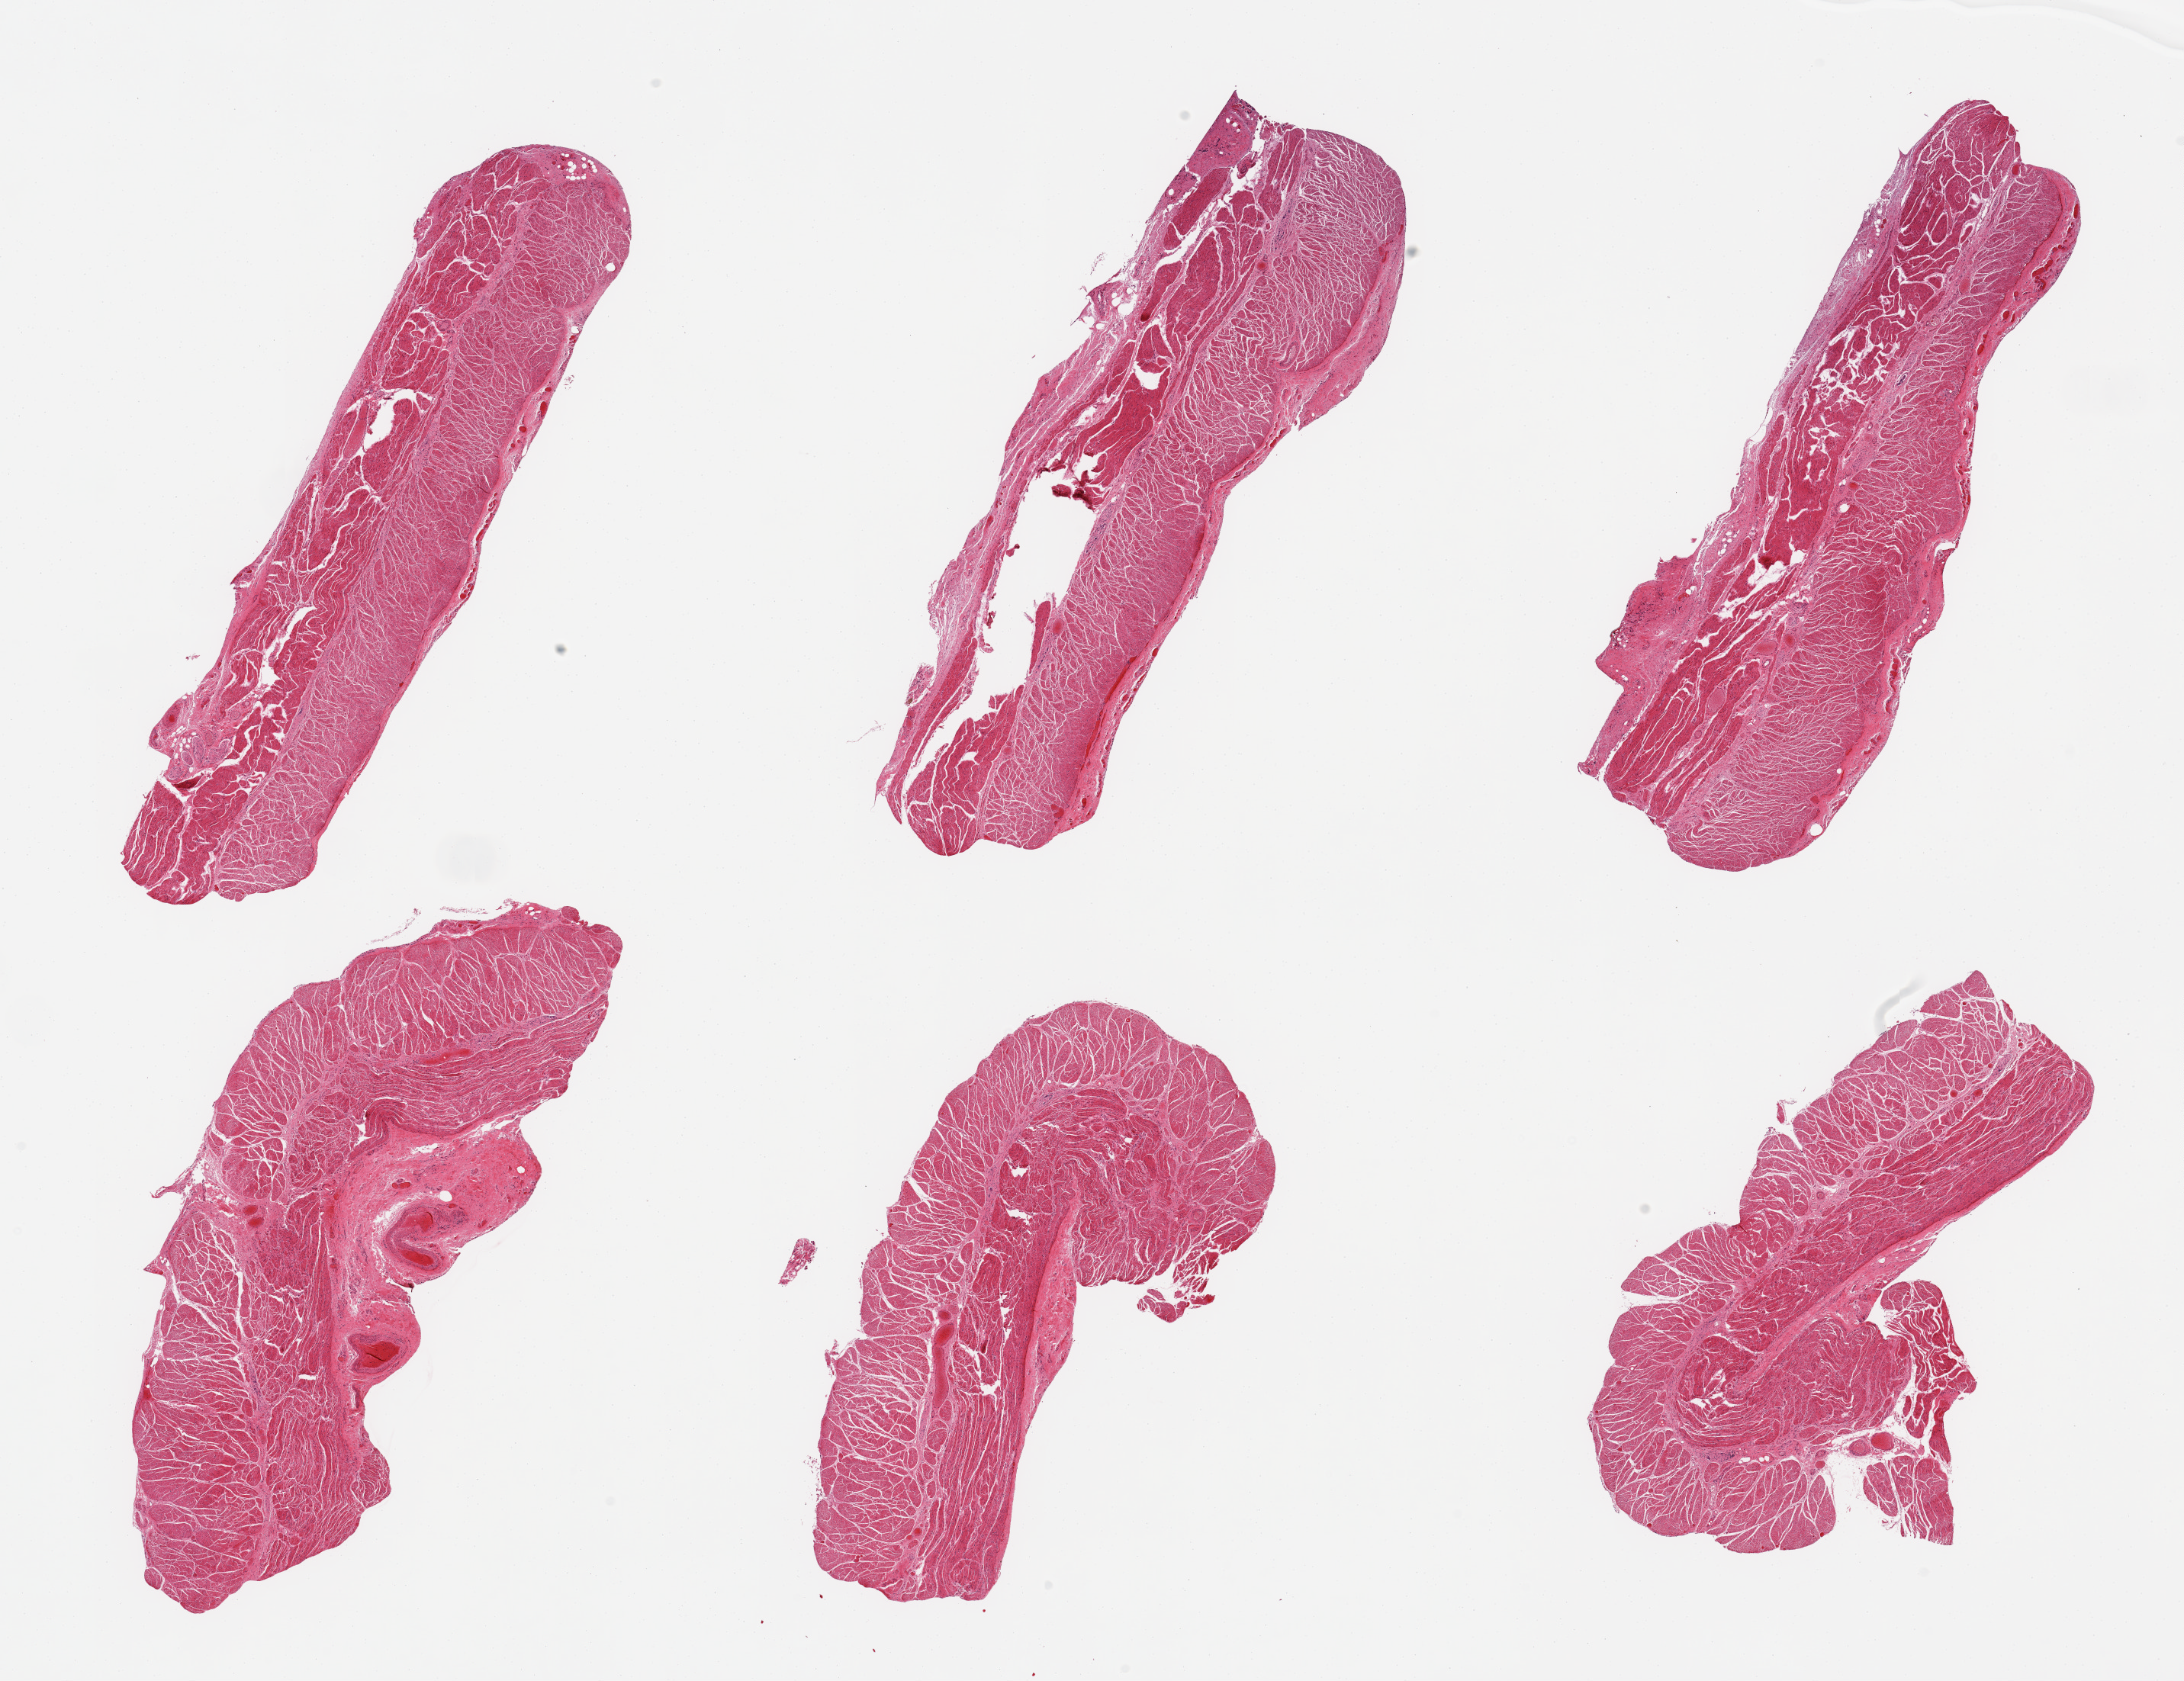
Digitized hematoxylin and eosin (H&E)-stained section, shown as a low-resolution overview of the whole scanned area (about 22.6 x 17.4 mm, acquisition: 20x scan), PAXgene-fixed paraffin-embedded (PFPE) section, section of gastroesophageal junction (target tissue), donor tissue sample. Donor sex: female.
Pathologist's review note for this sample: 6 pieces; 1 of 6 has 20% fibrovascular content on 1 side.